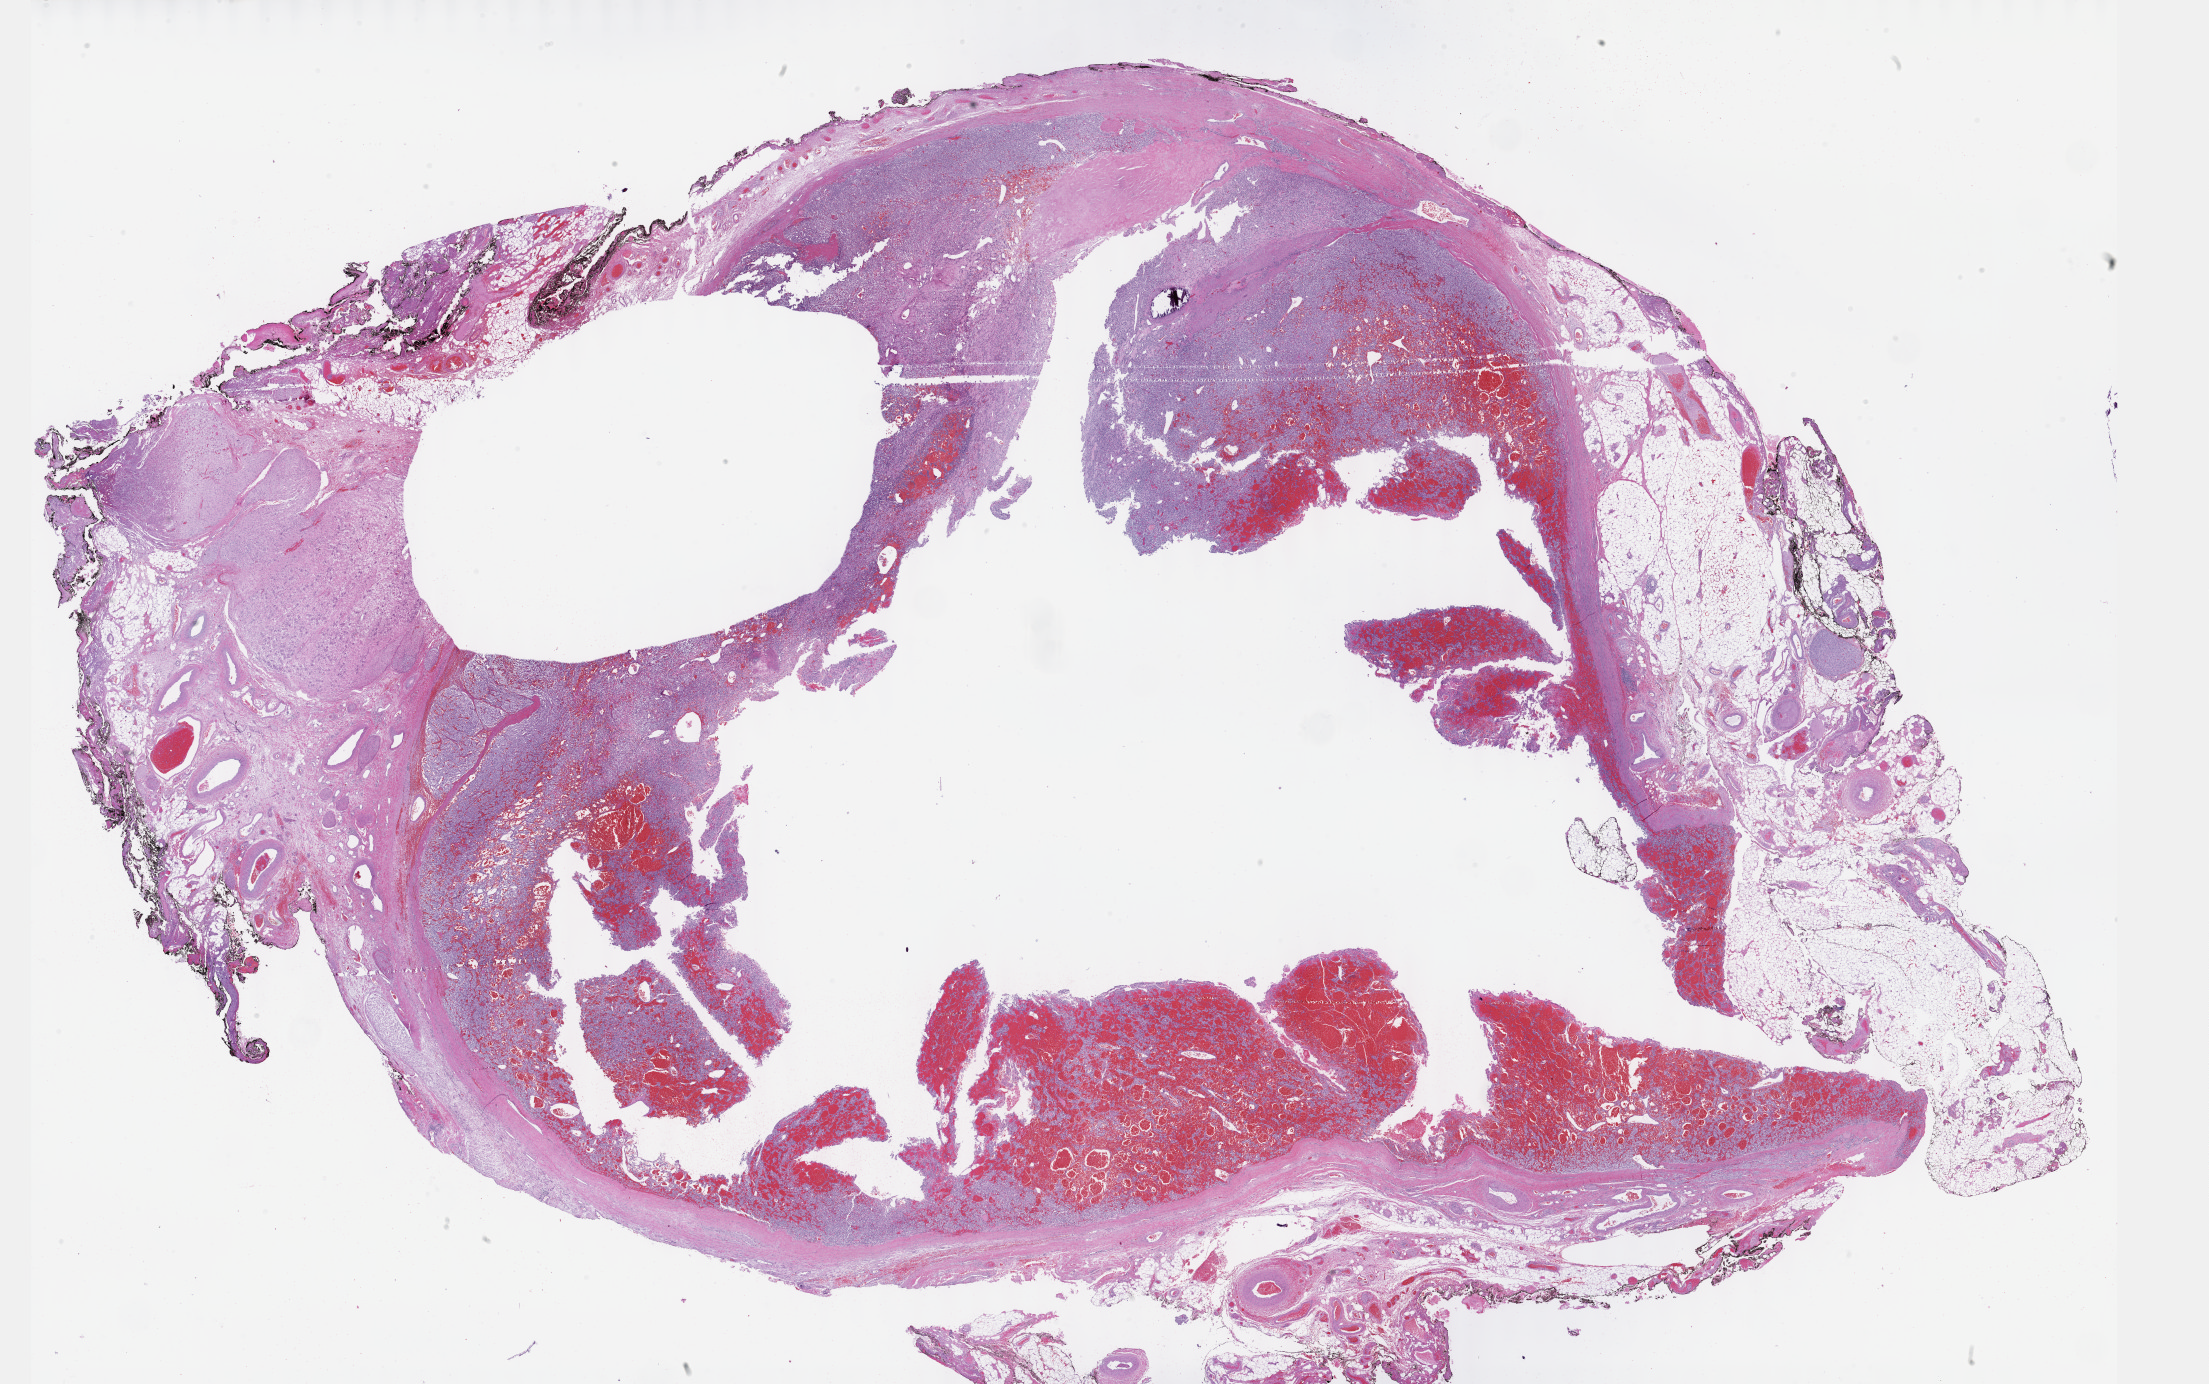
Hematoxylin and eosin (H&E) stained whole-slide image — low-resolution overview of the scanned area, about 35.7 x 22.4 mm, formalin-fixed paraffin-embedded (FFPE) diagnostic section, primary tumour sample from the adrenal gland. Female patient; age at initial diagnosis 42 years.
* laterality: right
* diagnosis: Pheochromocytoma, NOS